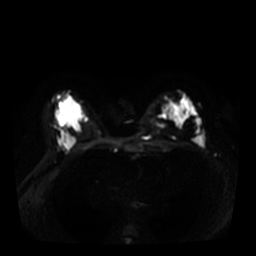
Breast MRI, one axial slice. Position 23 of 36 along the scan axis. Diffusion-weighted series; image 2 of 4 stored at this slice position (different b-values; order by instance number). 3 T. 5 mm slice thickness. 256 × 256 image matrix. Female patient.
Structures marked on this image (manually delineated by an expert):
- tumour on diffusion-weighted imaging: bounding box <159,116,166,118> (left, top, right, bottom; pixels)